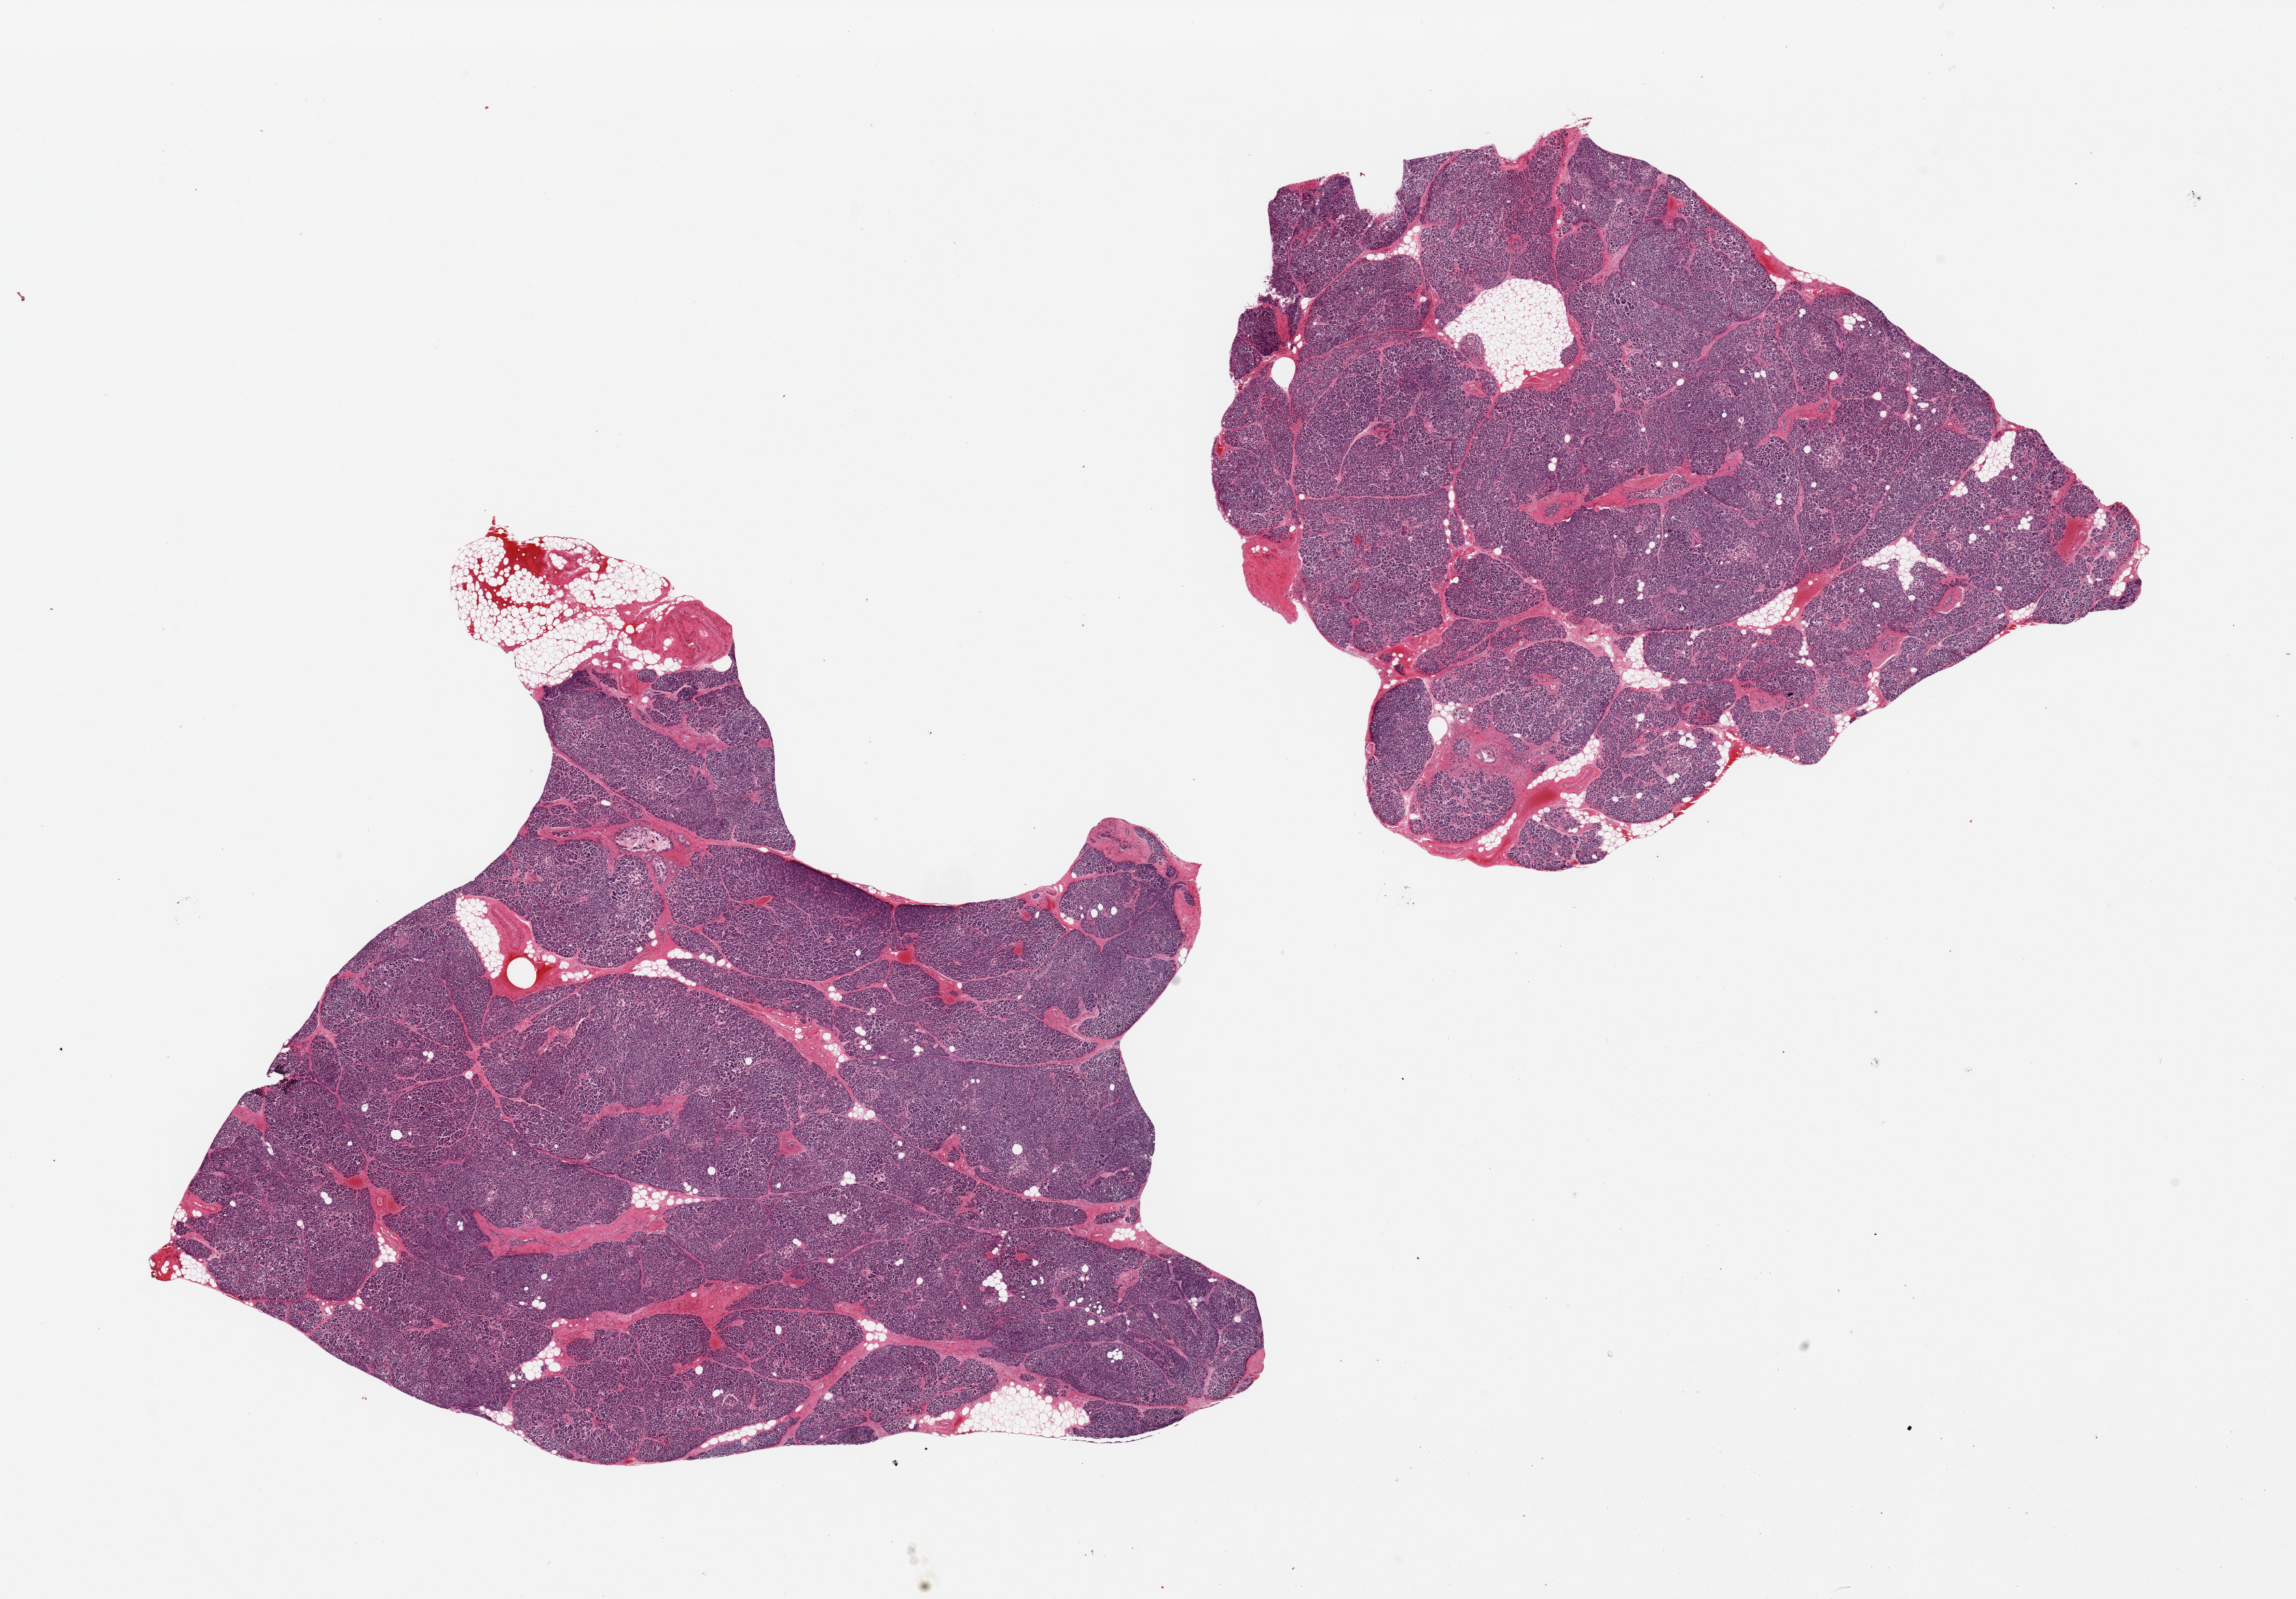
Hematoxylin and eosin (H&E) whole-slide image — low-resolution overview of the scanned area, about 26.6 x 18.5 mm (acquisition: 20x scan), PAXgene-fixed, paraffin-embedded tissue, target tissue: pancreas, donor tissue sample. Male donor.
Reviewer comment on this tissue sample: 2 pieces; 10% internal and external fat.